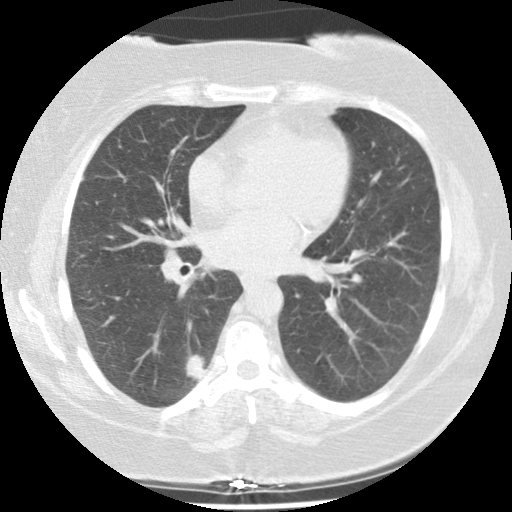
Axial slice from a low-dose chest CT screening exam, second annual screen, lung window (W 1500 / L -600 HU), standard (soft-tissue) reconstruction kernel (STANDARD). Female participant, aged 58 years at enrolment. Current smoker at enrolment.
• Expert reader's lesion annotation, bounding box (x1, y1, x2, y2) in pixels: (164, 335, 219, 399).
• The screening reader recorded 4 non-calcified nodules or masses ≥4 mm on this exam (right lower lobe, right middle lobe, right upper lobe, right middle lobe); which of them this box marks is not recorded.
• Official screen result: positive, other.
• Participant outcome: lung cancer diagnosed 299 days after this screen — adenocarcinoma, NOS, right lower lobe, stage IIIA (AJCC 6th edition), 25 mm at pathology.